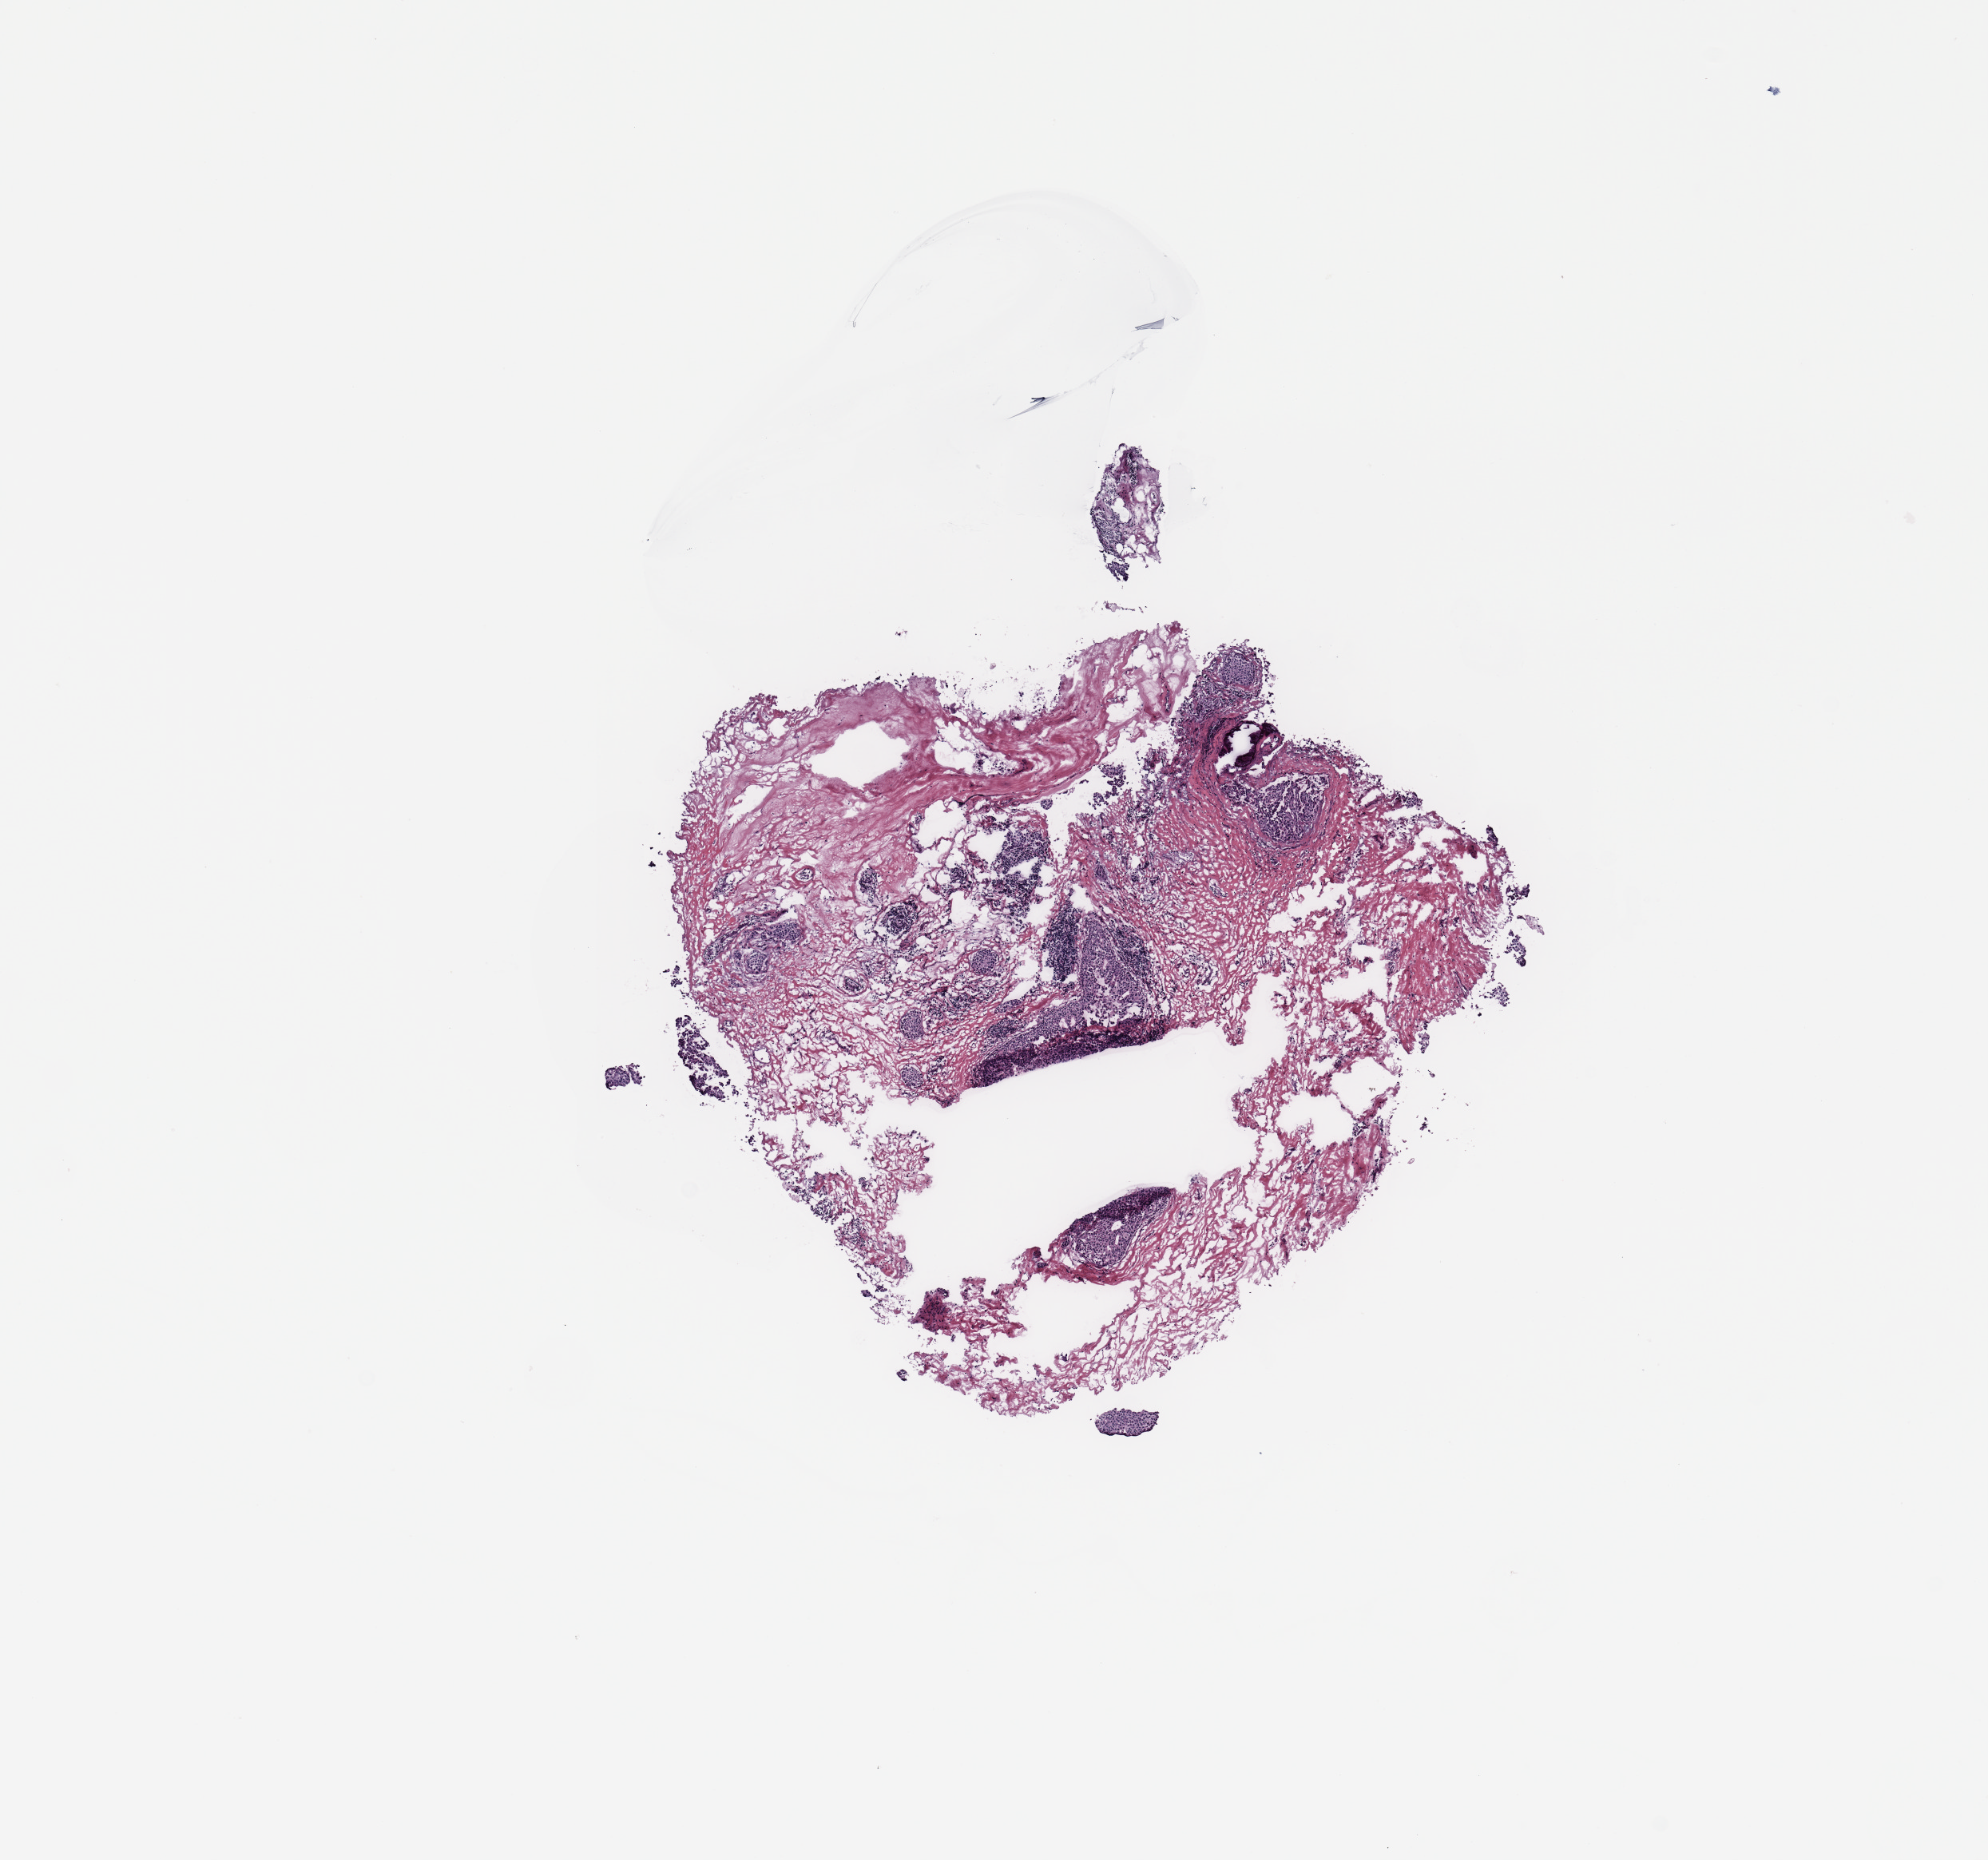
H&E whole-slide image, low-resolution overview of the scanned area, about 9.8 x 9.2 mm, breast, tissue type not recorded.
Patient diagnosis (cohort enrolment): breast cancer (breast).